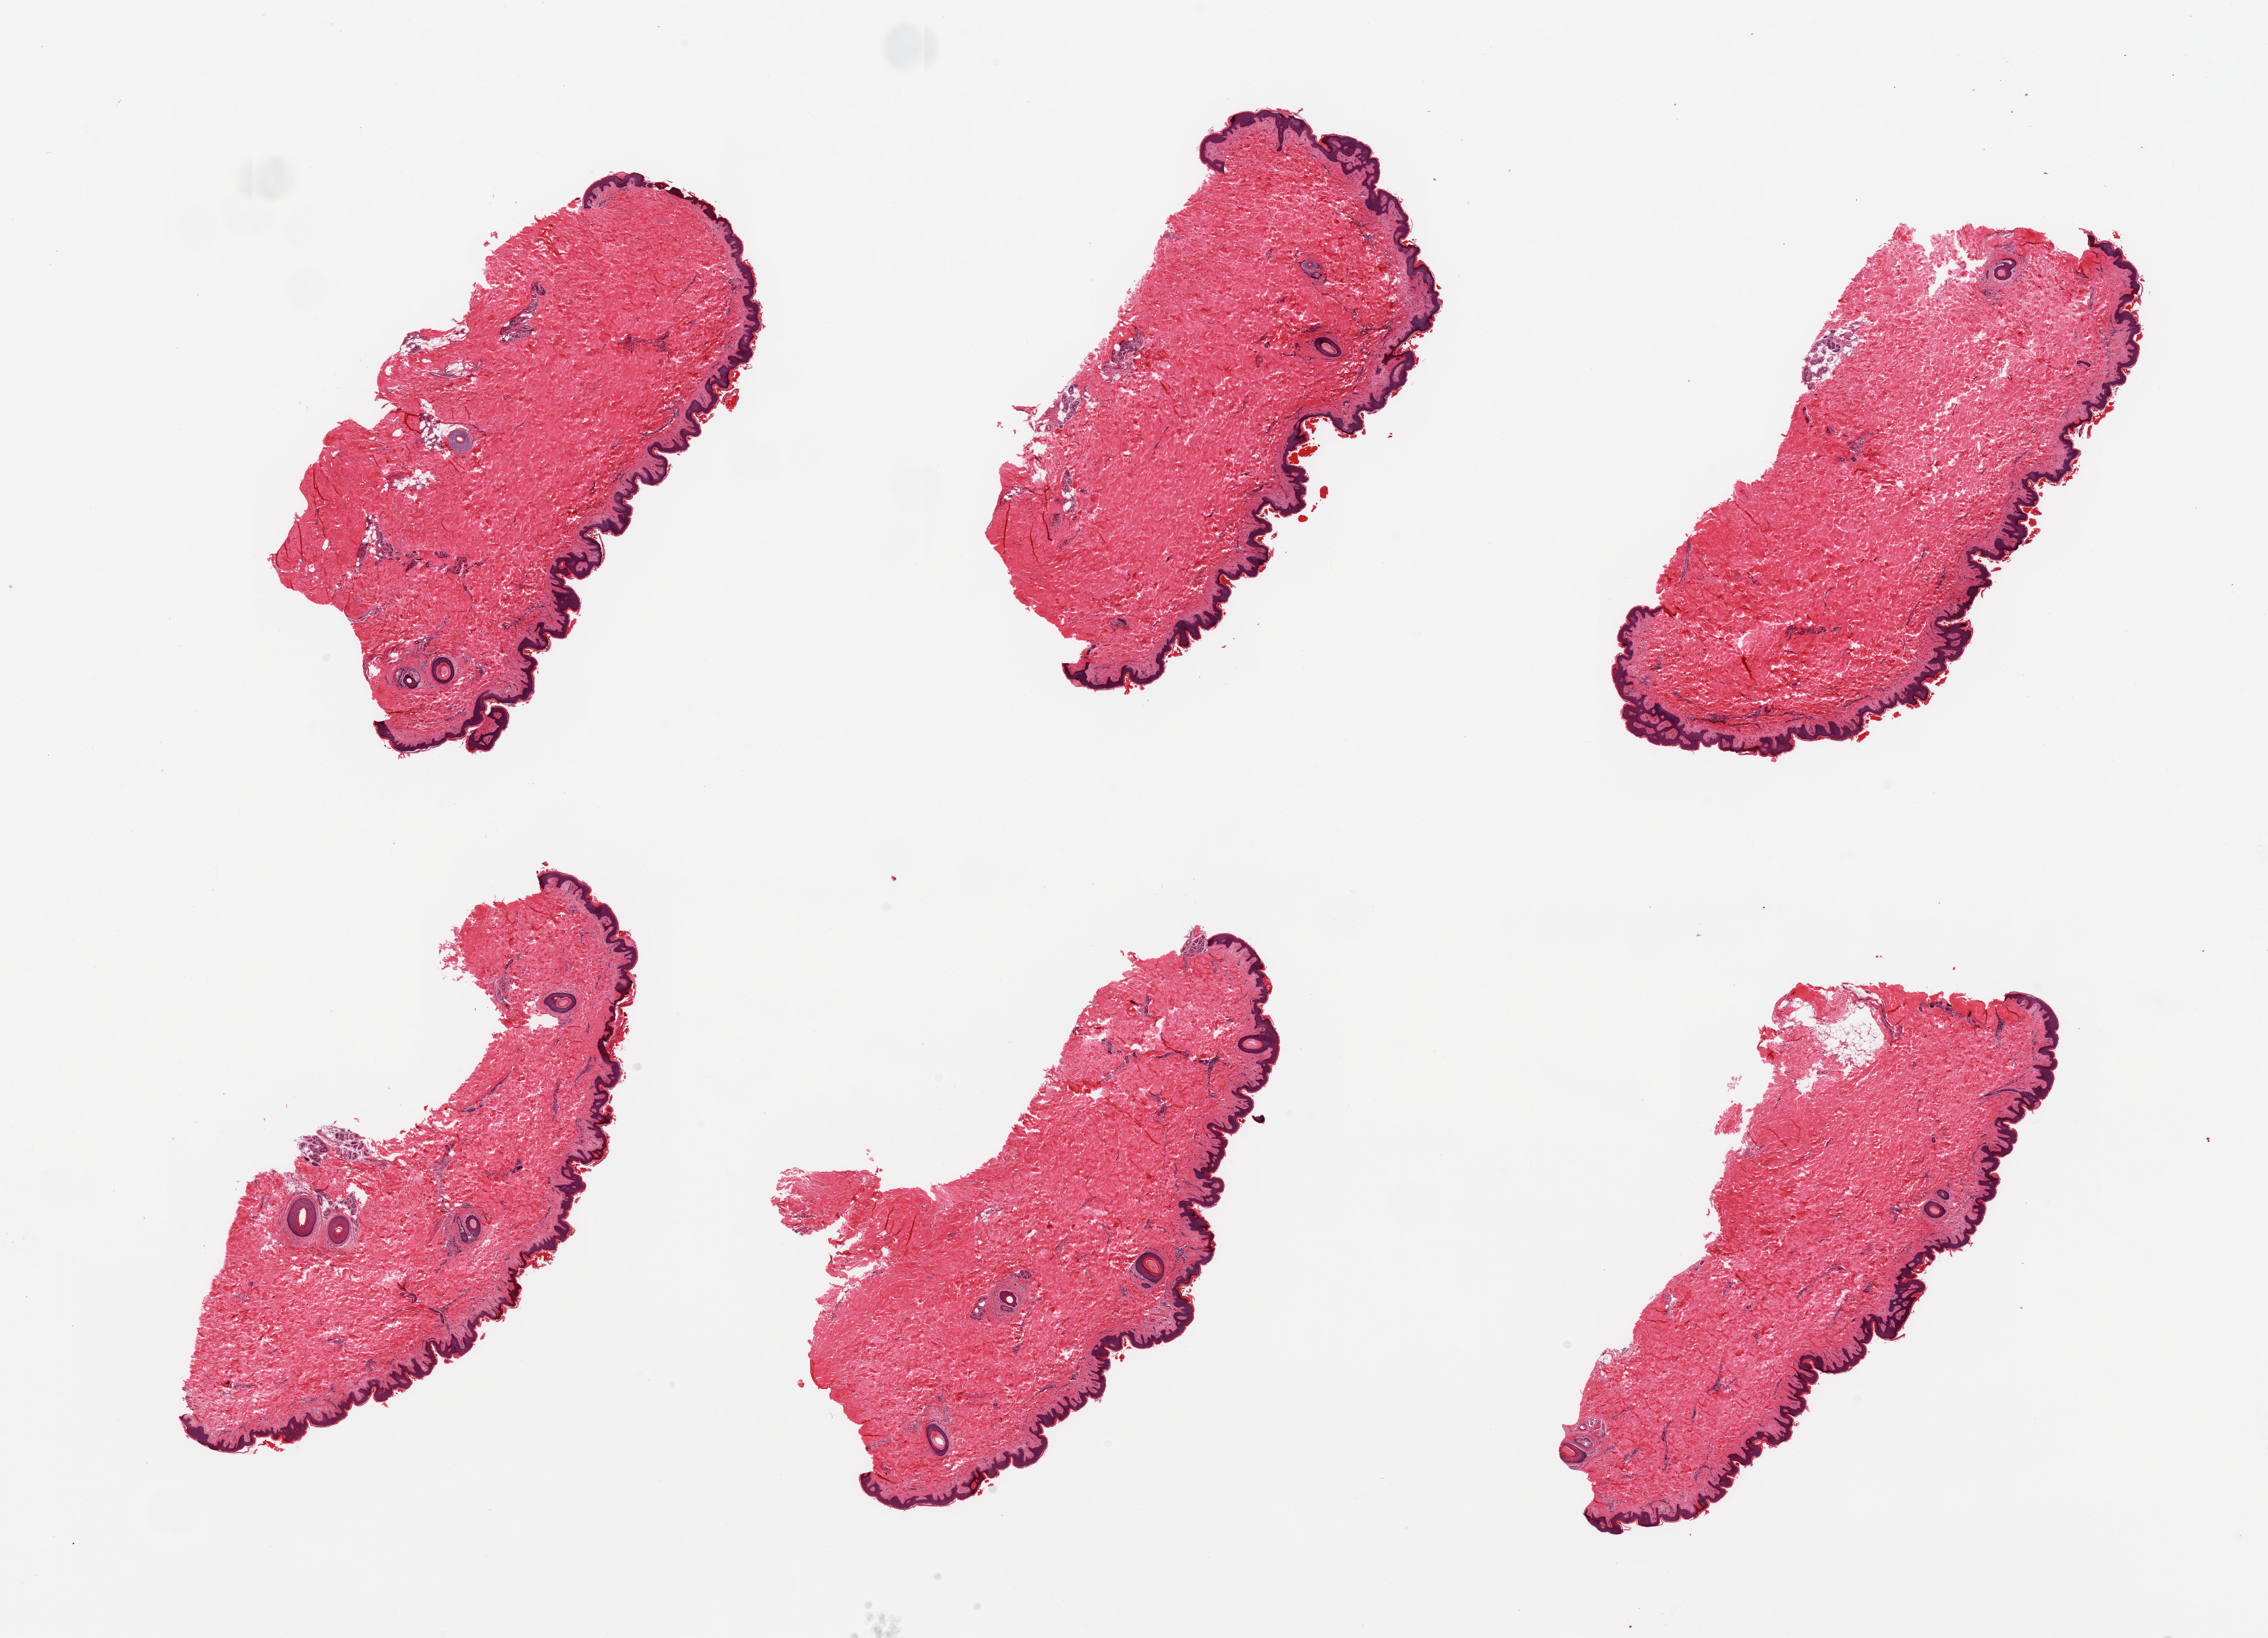
Whole-slide image, hematoxylin and eosin (H&E) stain, brightfield, low-resolution overview of the scanned area, about 26.6 x 19.2 mm (acquisition: 20x scan), PAXgene-fixed, paraffin-embedded tissue, target tissue: skin of suprapubic region, tissue donor sample. Donor sex: male.
• review note (as recorded): 6 pieces, minimal dermal fat; squamous epithelium is ~50-60 microns